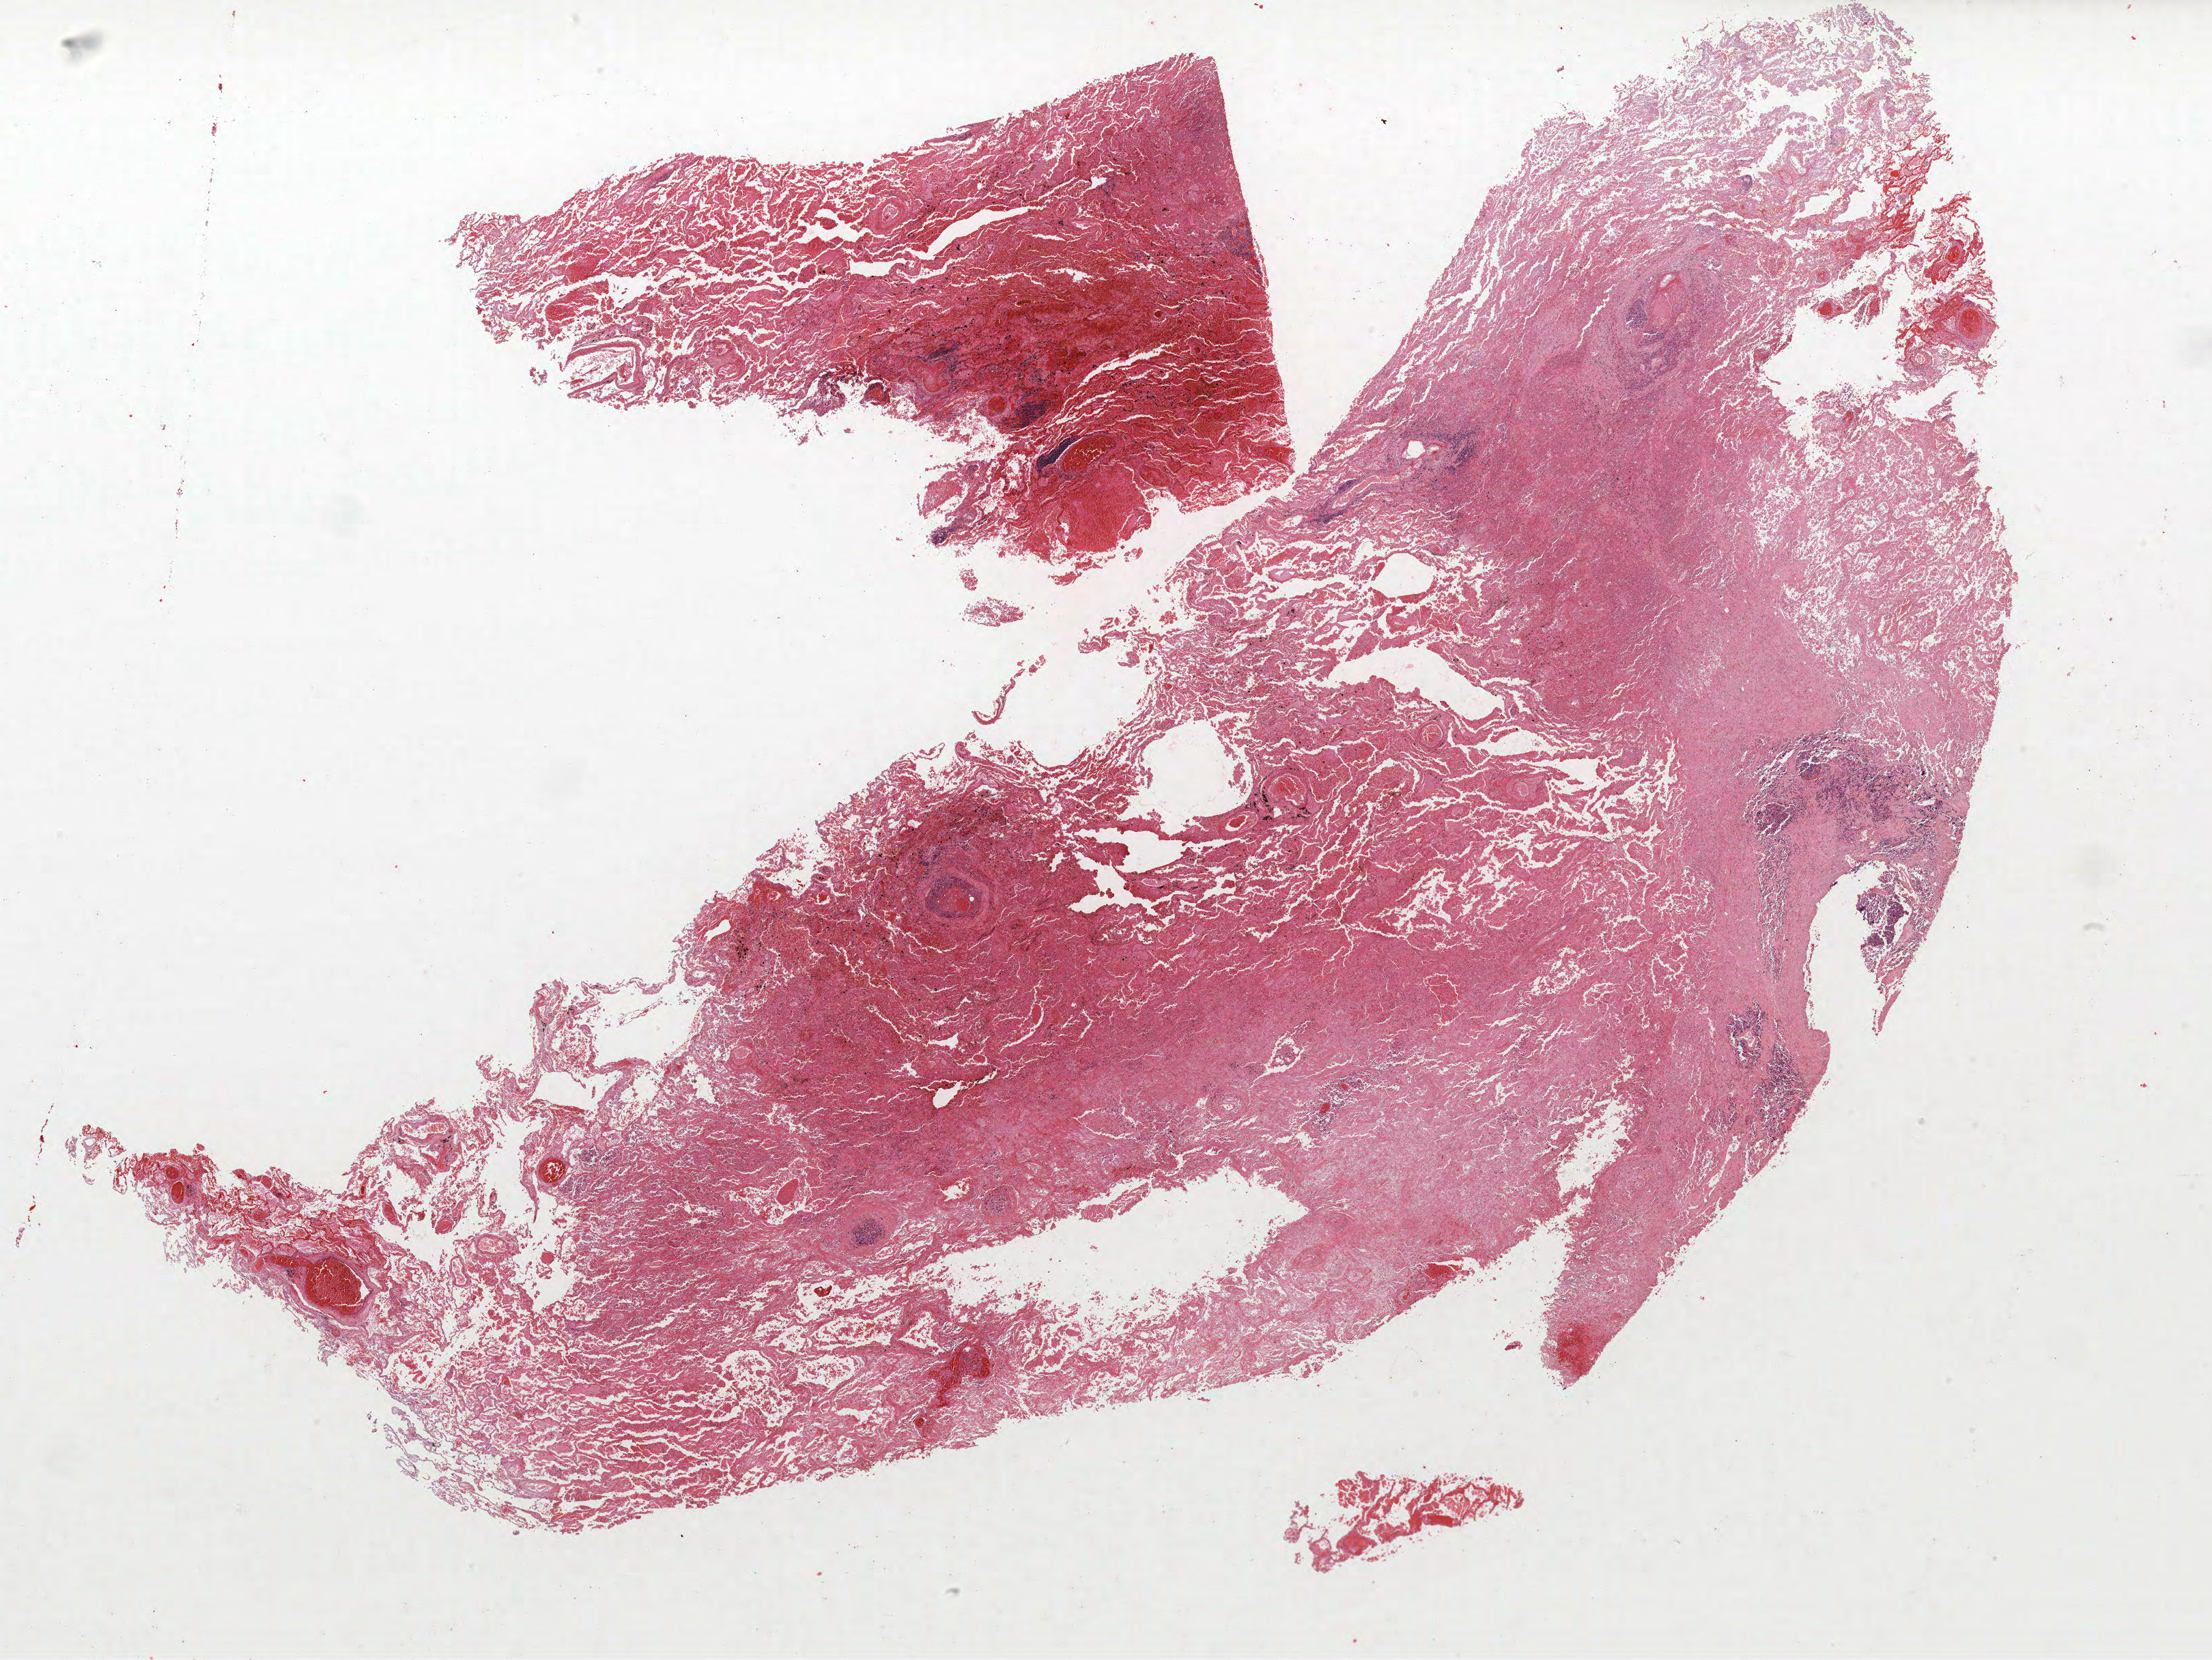
Whole-slide histology image, H&E — whole scanned area (about 25.9 x 19.5 mm, acquisition: 40x scan) shown as a low-resolution overview; formalin-fixed paraffin-embedded (FFPE) section; lung tissue. Male patient, aged 67 at enrolment. Current smoker at enrolment.
* participant's lung-cancer diagnosis: Small cell carcinoma, NOS
* stage (AJCC 6th edition): IA
* ICD-O-3 topography: middle lobe of lung (C34.2)
* primary tumour location (clinical record): right middle lobe
* tumour size (pathology): 20 mm